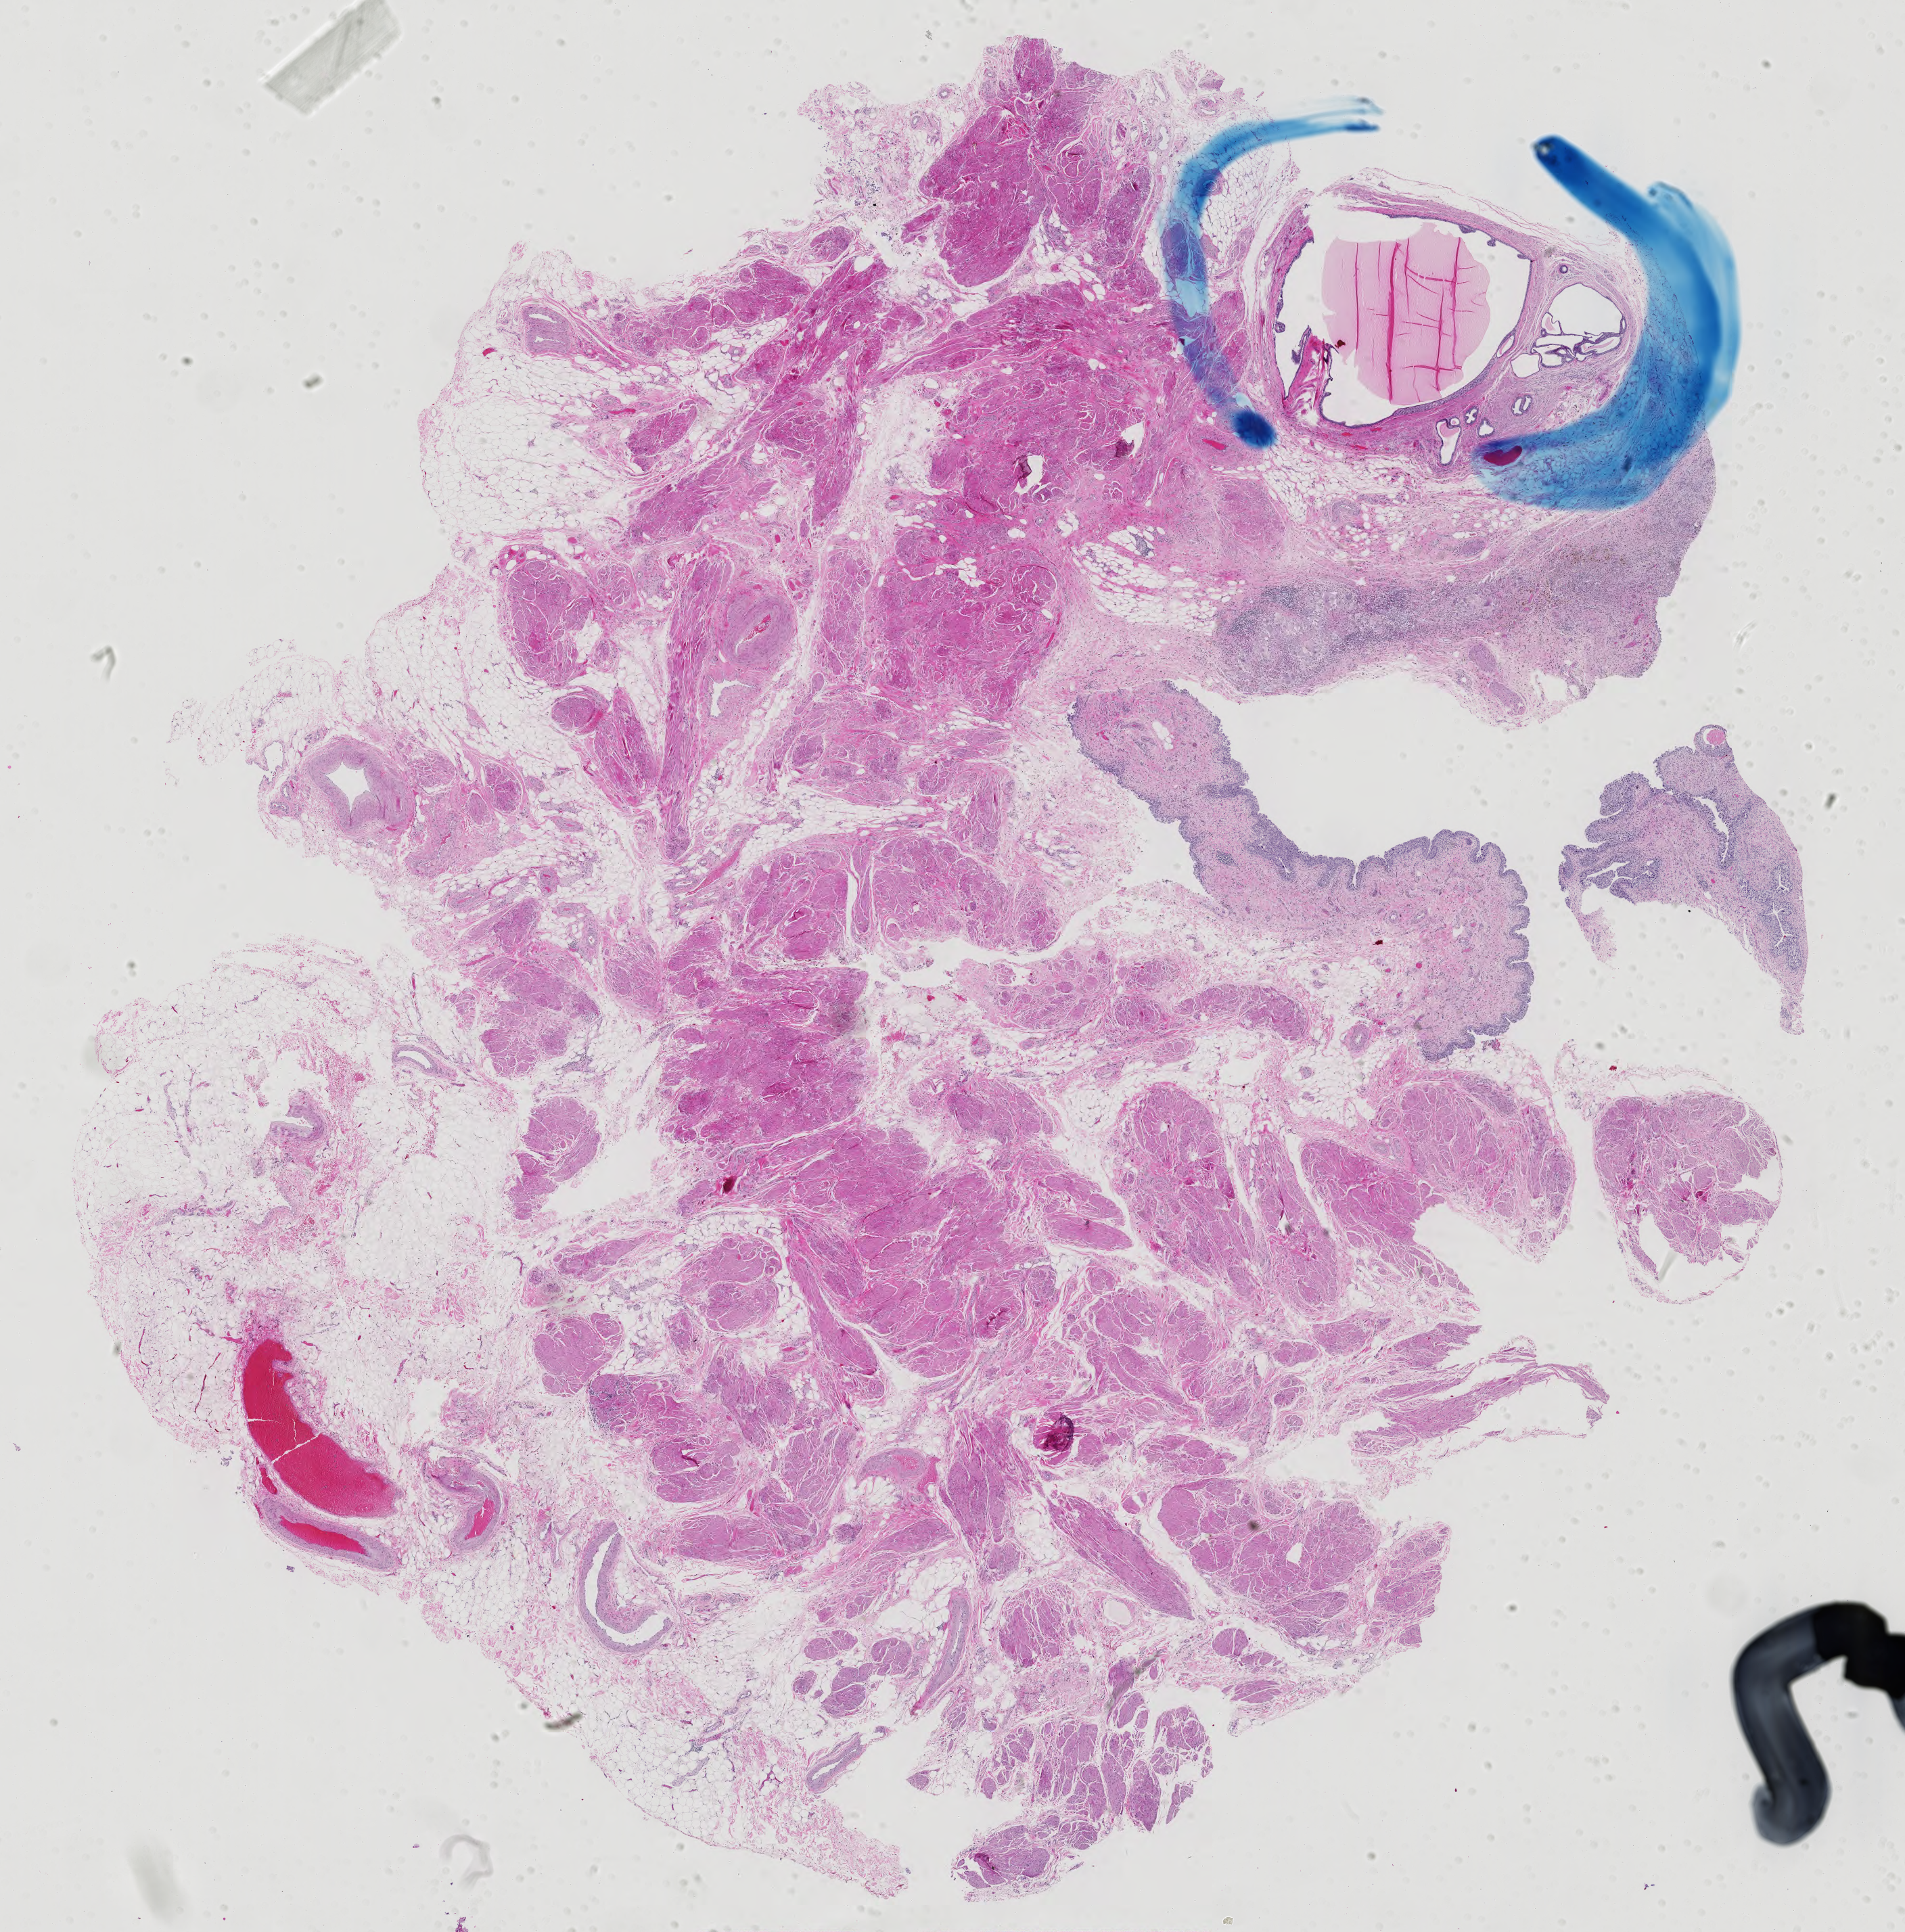
H&E-stained whole-slide image, whole scanned area (about 20.5 x 20.8 mm) shown as a low-resolution overview. Formalin-fixed paraffin-embedded (FFPE) diagnostic section. Primary tumour sample from the bladder. Patient: female, age at initial diagnosis 67 years. Histologic grade: high grade.
* TNM: T3b N0 MX
* diagnosis: Transitional cell carcinoma
* lymph nodes positive (case pathology): 0 of 16 examined
* AJCC pathologic stage: III (7th edition)